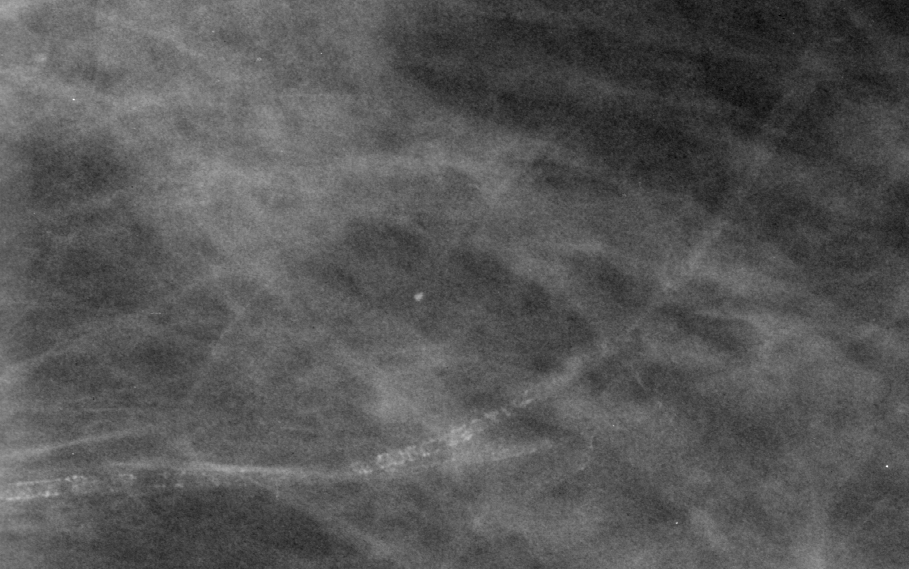
Region of interest cut from a scanned film mammogram (one marked finding); left breast; CC view.
Calcifications, morphology vascular / coarse / lucent centered; BI-RADS assessment category 2; subtlety rating 5 on a 1 (subtle) to 5 (obvious) scale; benign without callback (not worked up further).